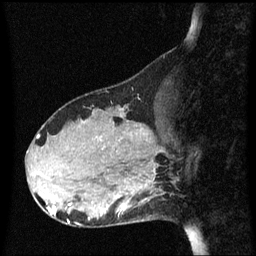
Breast MRI (dynamic contrast-enhanced), one sagittal slice; slice 19 of 60 in the series (ordered by position); dynamic contrast-enhanced series, image 2 of 3 at this slice position (ordered by acquisition); 1.5 T; TE 4.2 ms, TR 8.4 ms; 2.1 mm slice thickness; 256 × 256 image matrix, field of view 210 × 210 mm. Patient: female, 31 years. From the clinical record (not read from this slice): setting: breast cancer imaged before/during neoadjuvant chemotherapy; receptor status: HR-positive, HER2-negative.
Annotated regions visible in this slice (semi-automatically segmented with operator editing):
- analysis volume of interest (the breast-tissue region the enhancement analysis was run in; not a lesion): box from (x=98, y=175) to (x=165, y=228) px
- tumour enhancement mask (voxels above the 70 % enhancement threshold inside the analysis volume of interest): (x=122, y=185)–(x=148, y=211)